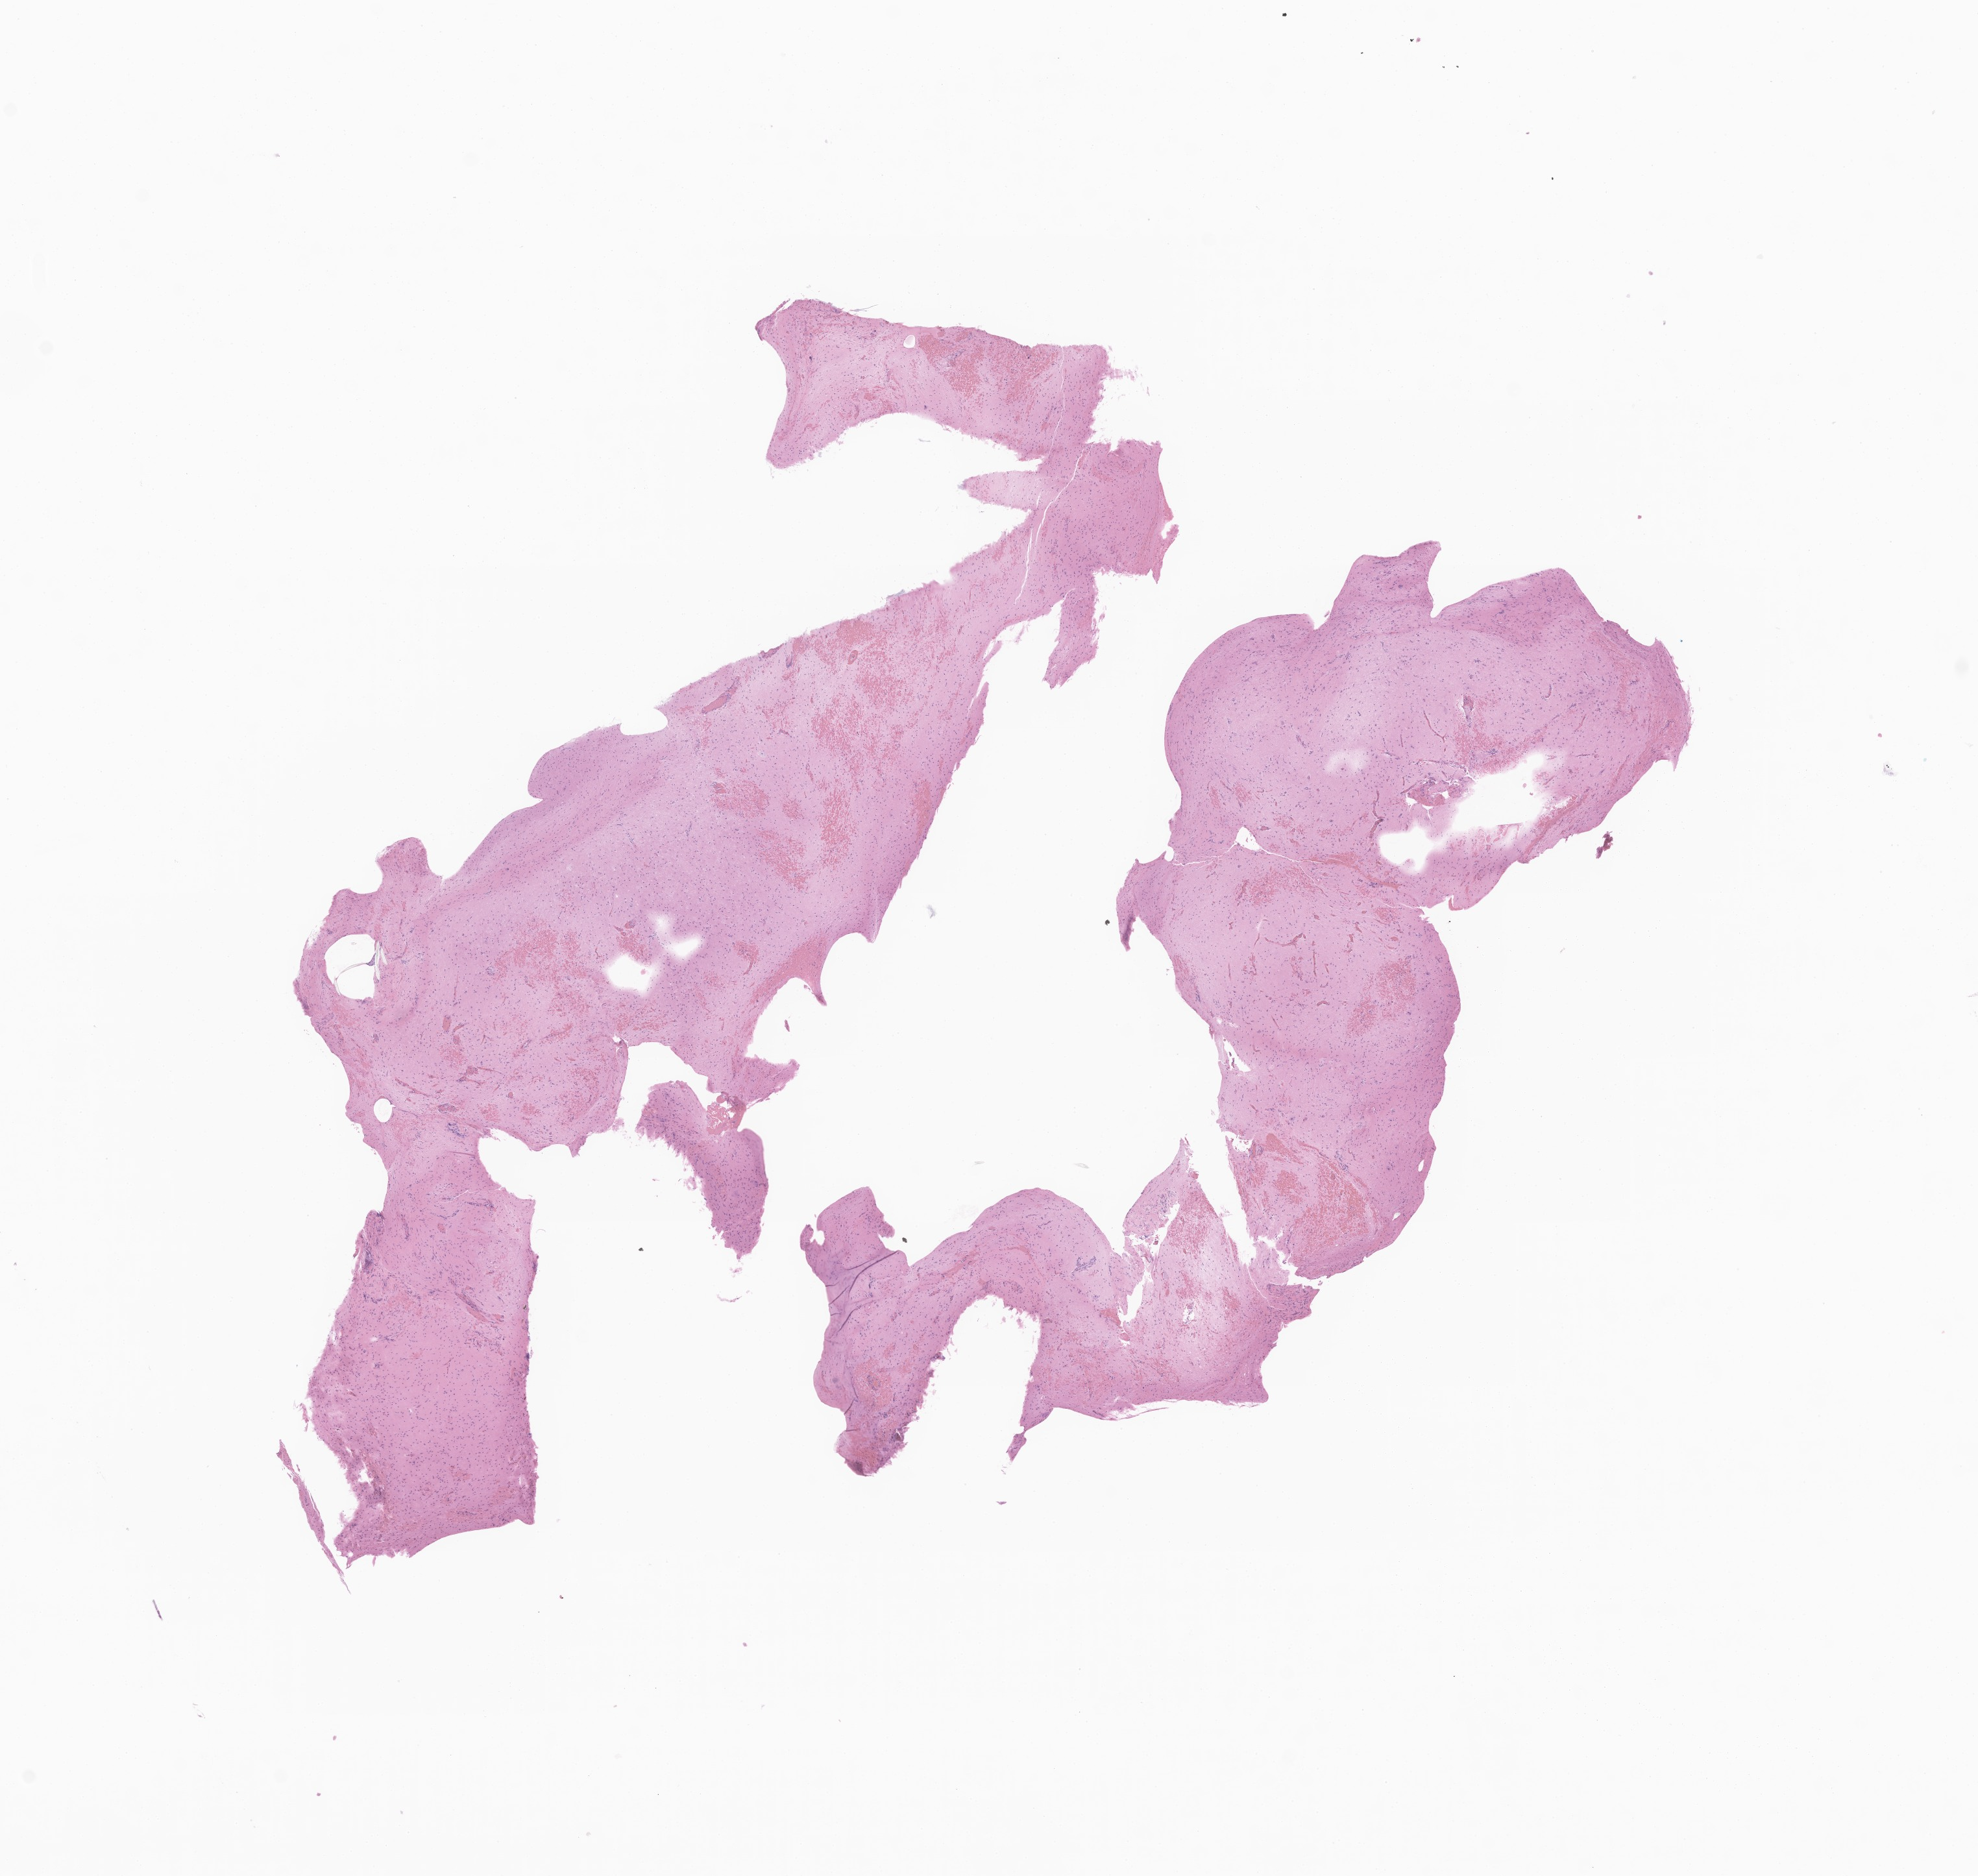
Haematoxylin and eosin whole-slide image of tumor tissue from the brain — whole scanned area (about 12.9 x 12.2 mm) shown as a low-resolution overview; FFPE section. Male patient, age 344 days.
Diagnosis (ICD-O-3 morphology term): Neoplasm, uncertain whether benign or malignant.